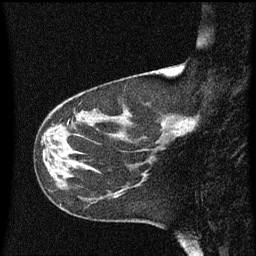
Breast MRI (dynamic contrast-enhanced), one sagittal slice; position 22 of 60 along the scan axis; dynamic contrast-enhanced series, image 2 of 3 at this slice position (ordered by acquisition); 1.5 T; TE 4.2 ms, TR 8.4 ms; 2 mm slice thickness; 256 × 256 image matrix, field of view 200 × 200 mm. Female patient, age 41 years. From the clinical record (not read from this slice): setting: breast cancer imaged before/during neoadjuvant chemotherapy; receptor status: triple-negative.
Structures marked on this image (semi-automatic segmentation, software-assisted and operator-edited):
- analysis volume of interest (the breast-tissue region the enhancement analysis was run in; not a lesion): box from (x=158, y=104) to (x=202, y=145) px
- tumour enhancement mask (voxels above the 70 % enhancement threshold inside the analysis volume of interest): (x=189, y=120)–(x=197, y=133)